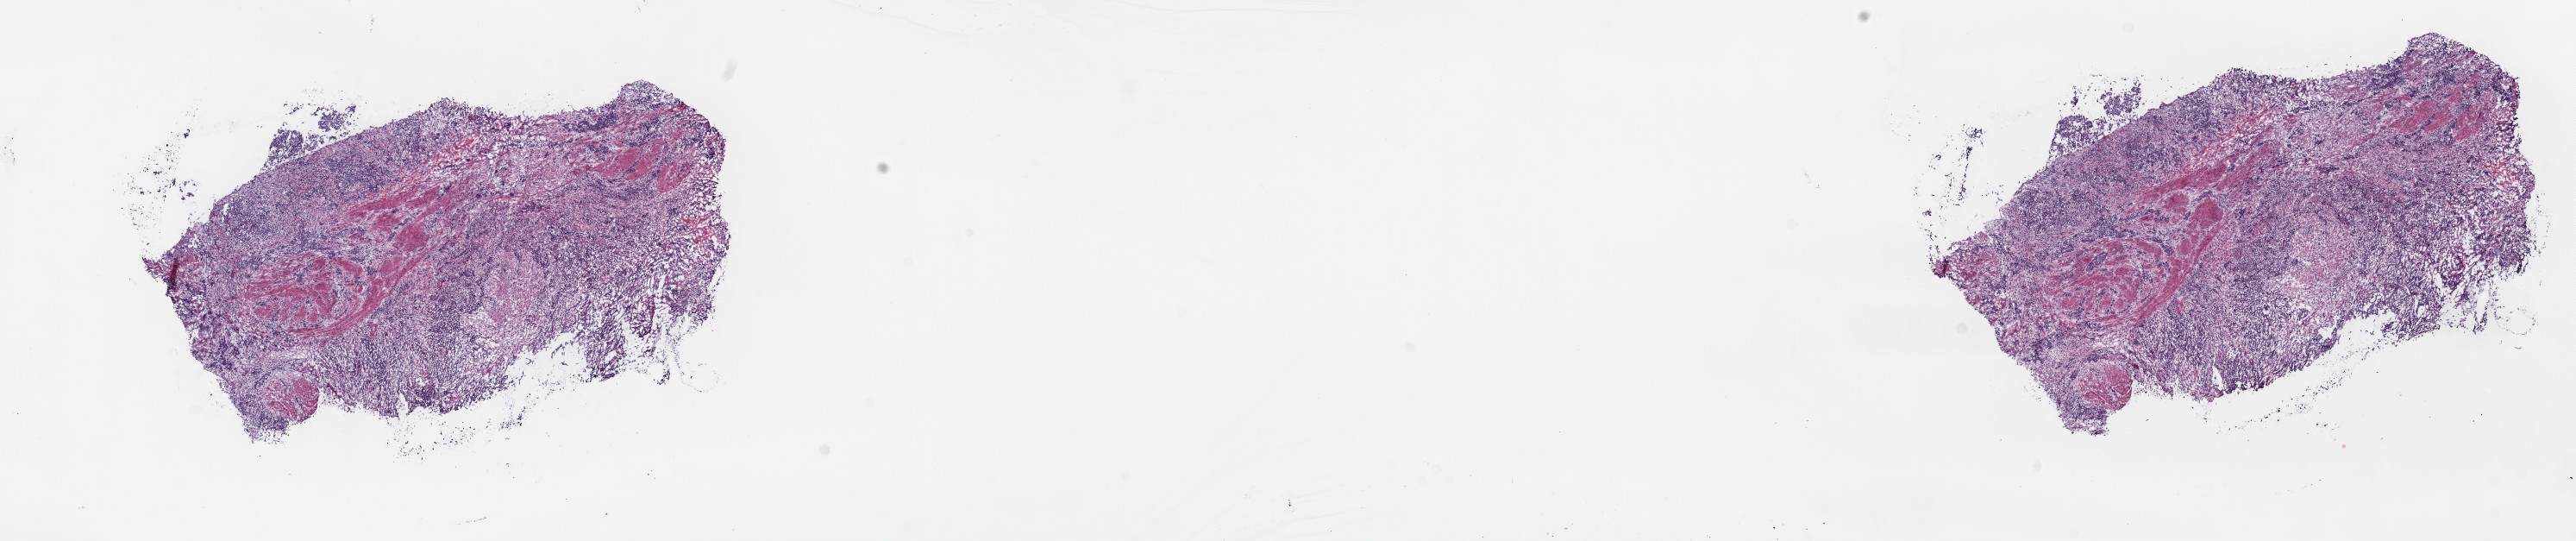
Whole-slide histology image, H&E-stained — low-resolution overview of the scanned area, about 24.2 x 5.1 mm (slide scanned at 40x), frozen section from the top of the tissue portion, primary tumour sample from the bladder. Male, age 63 years at initial diagnosis. Histologic grade: high grade. Pathologist review of this section (percent, as recorded): tumour cells 100%, tumour nuclei 65%, normal cells 0%, stromal cells 0%, necrosis 0%. Infiltration values recorded for this section: lymphocyte infiltration 4%, monocyte infiltration 0%, neutrophil infiltration 0%.
Diagnosis: Transitional cell carcinoma (posterior wall of bladder). TNM: T3 N1 M0. AJCC pathologic stage: IV (6th edition). Lymph nodes positive (case pathology): 1 of 18 examined.